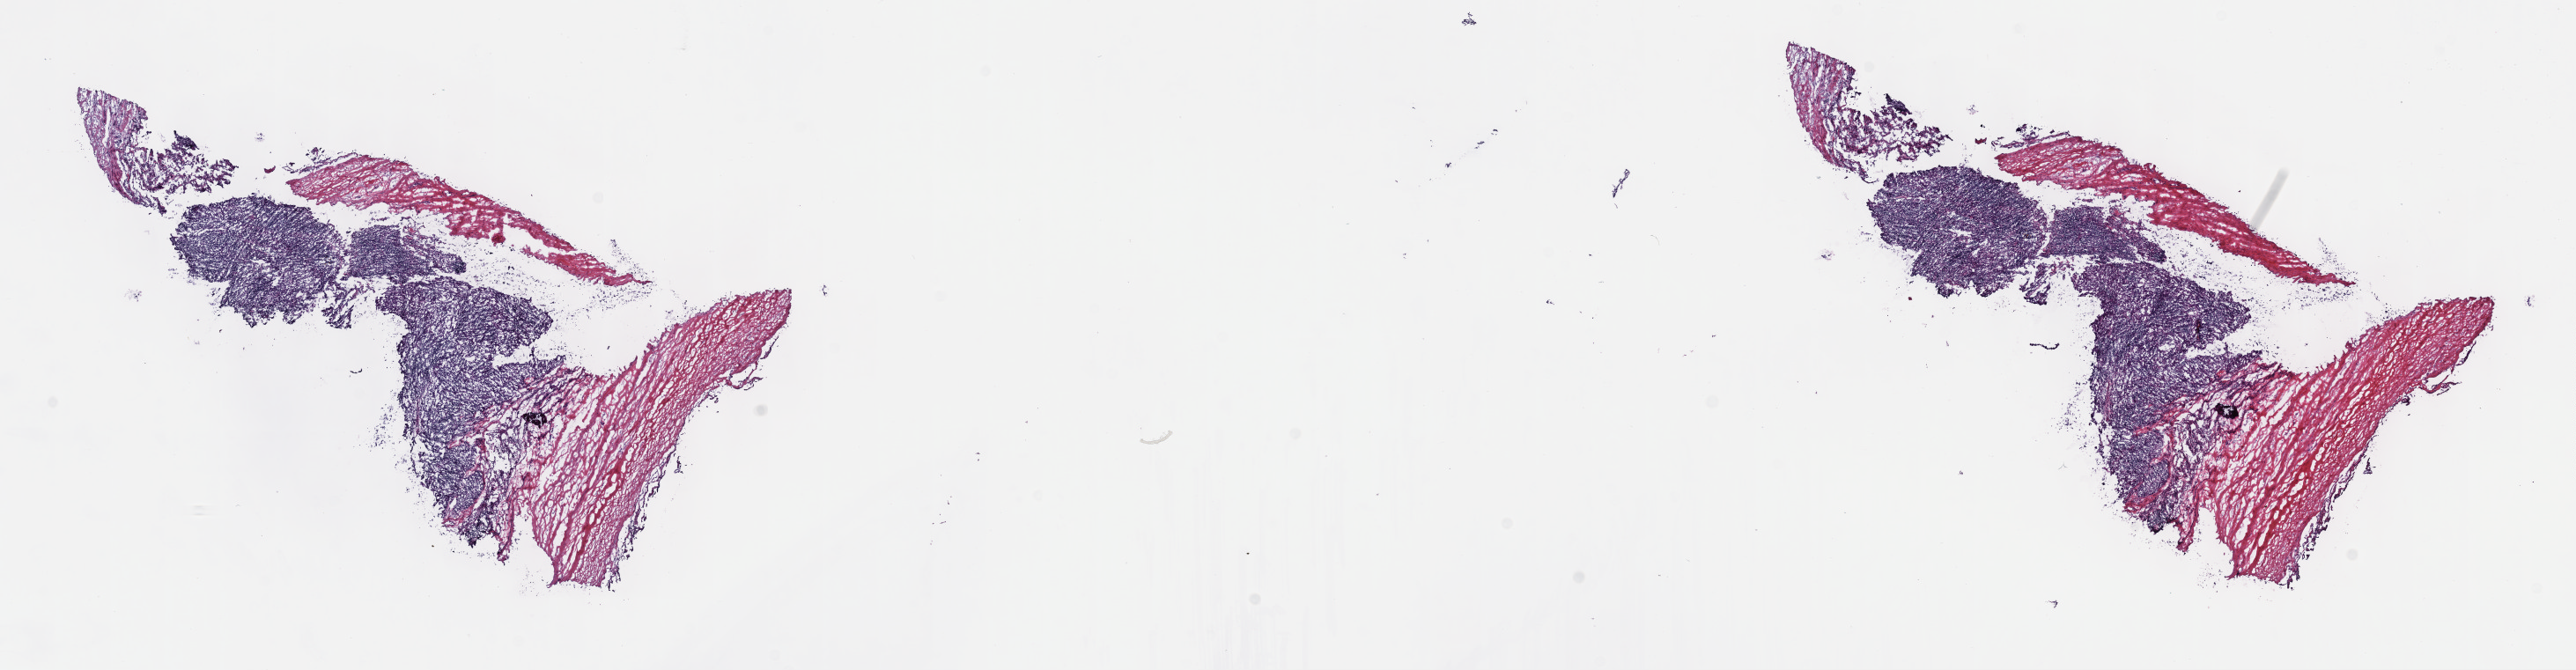
Whole-slide histology image, H&E-stained, whole scanned area (about 23.7 x 6.2 mm) shown as a low-resolution overview; frozen section from the top of the tissue portion; sample: primary tumour, thymus. Male, age 17 years at initial diagnosis. Slide review estimates, as recorded: tumour cells 60%, tumour nuclei 70%, normal cells 40%, stromal cells 0%, necrosis 0%. Inflammatory infiltration, as recorded: lymphocyte infiltration 2%, monocyte infiltration 0%, neutrophil infiltration 0%.
- pathologic diagnosis: Thymoma, type B2, malignant